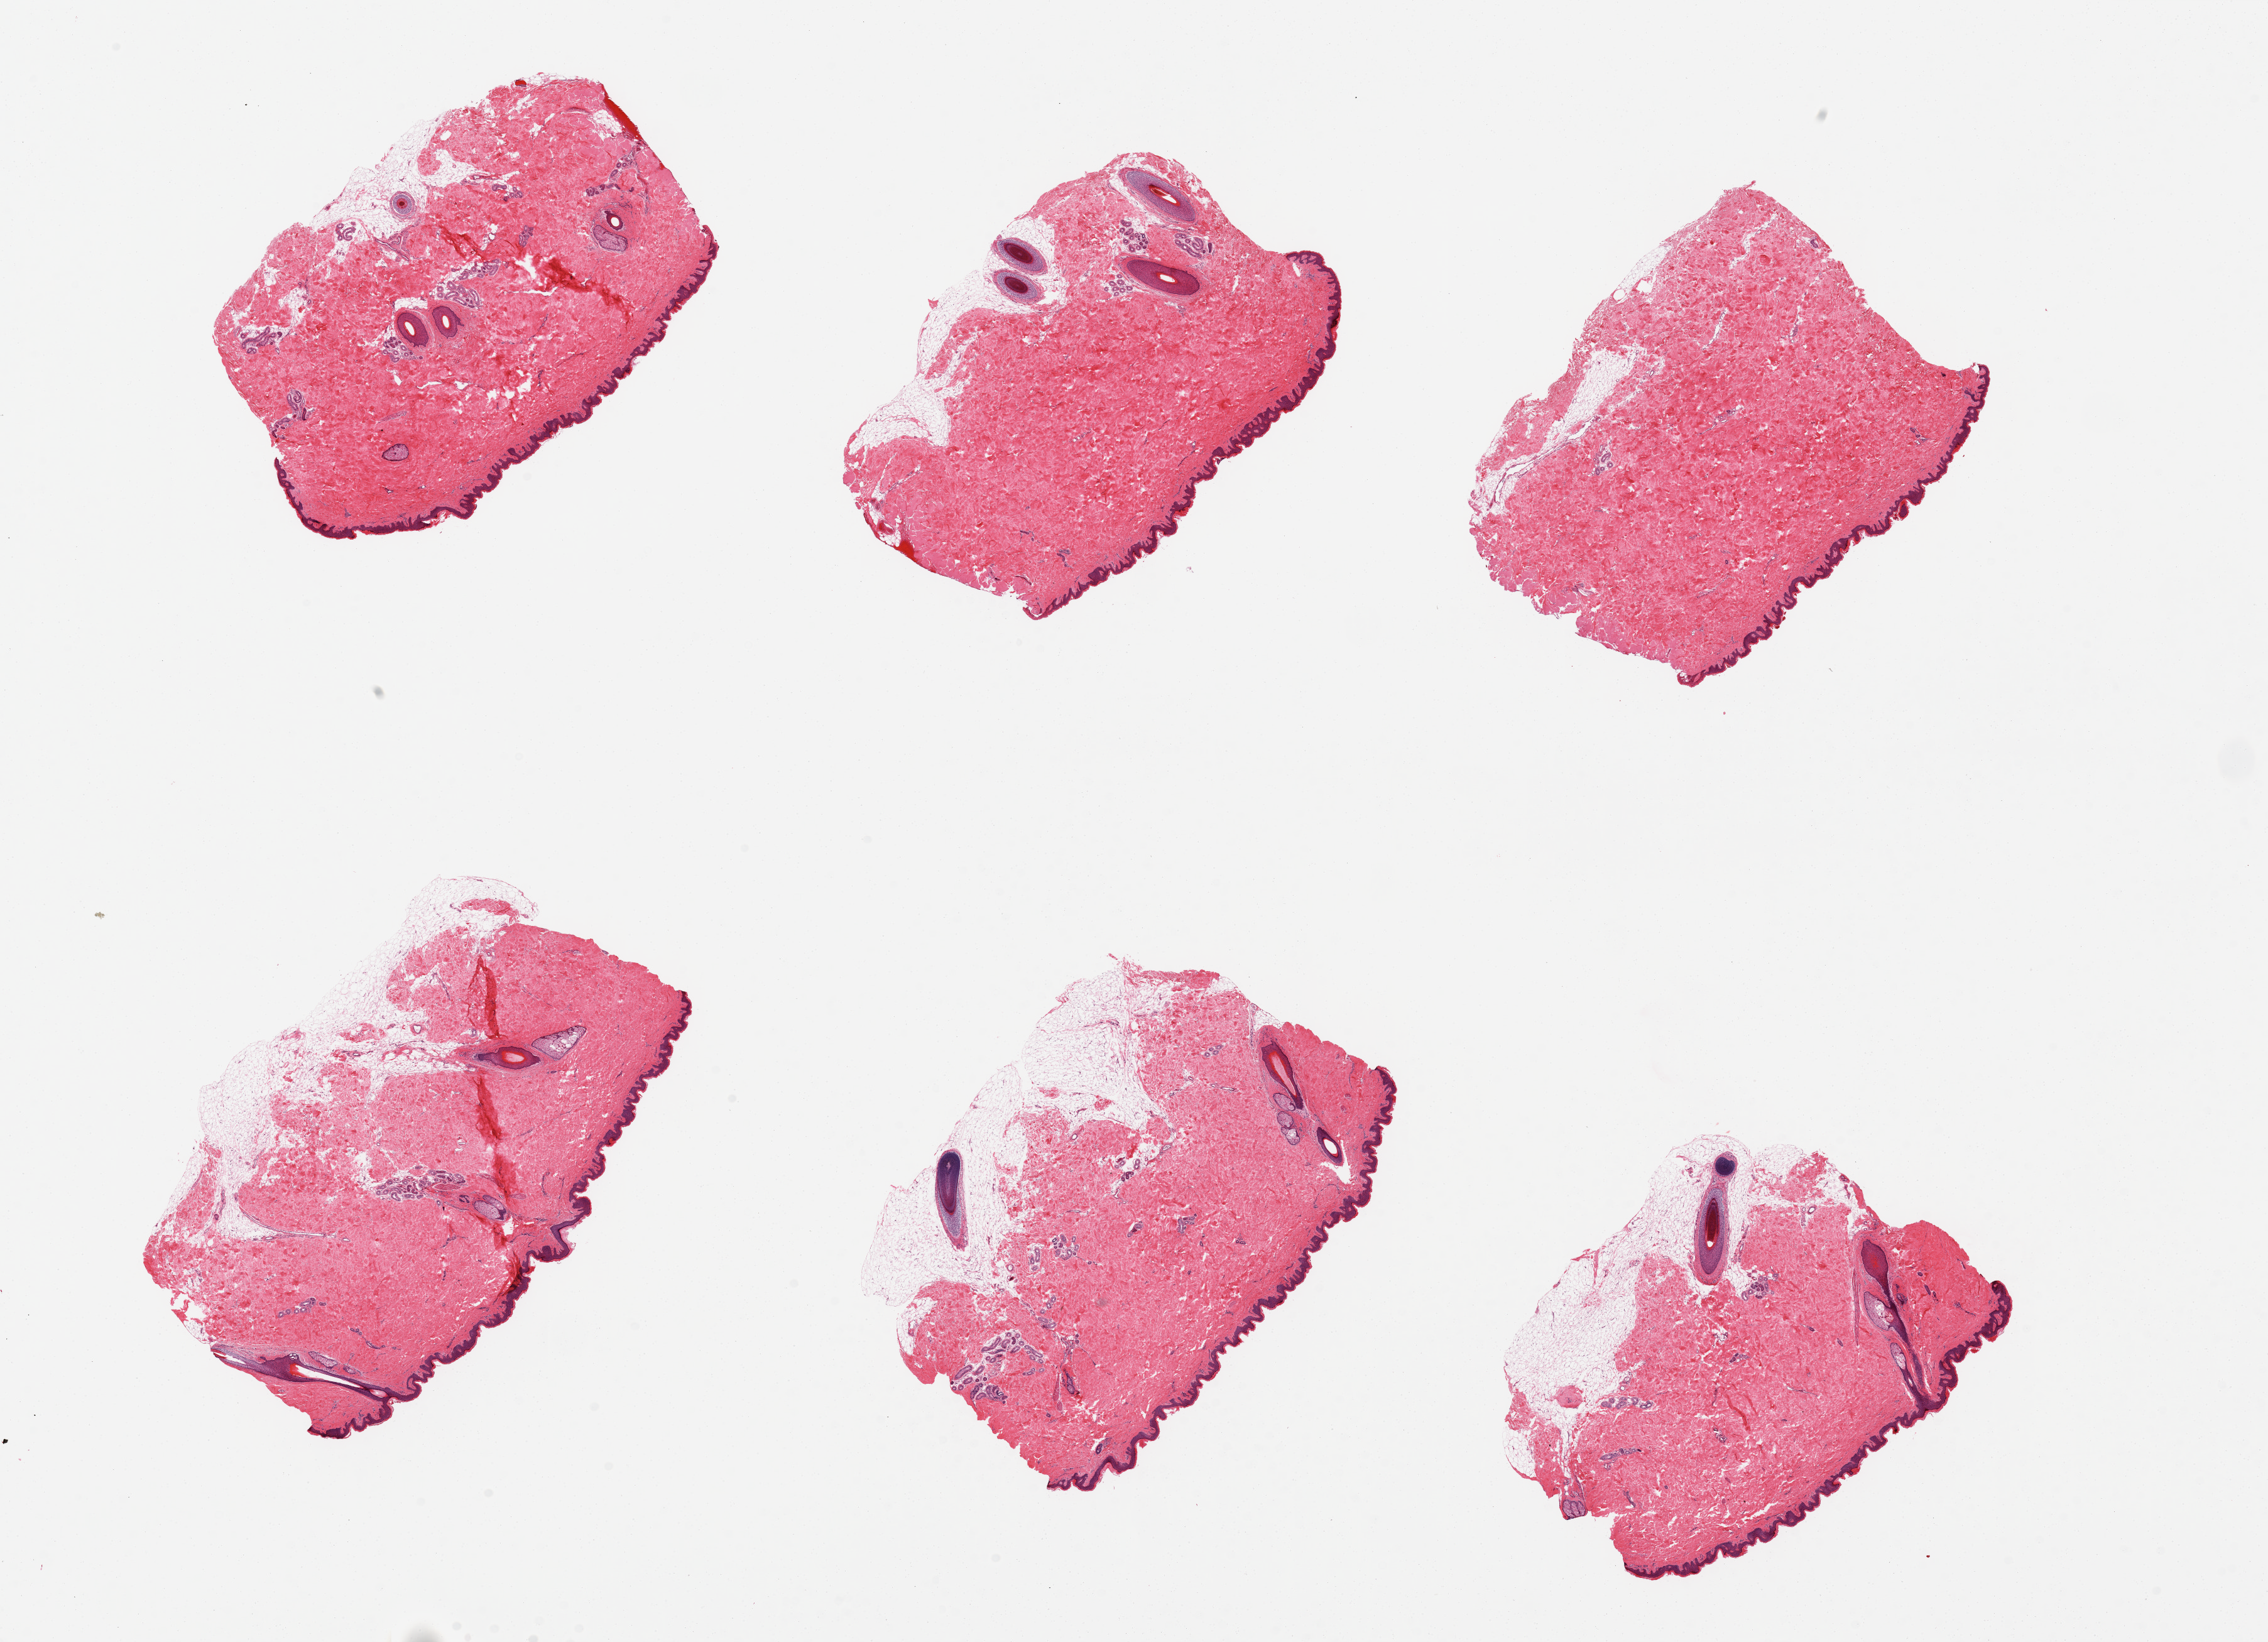
Digitized haematoxylin and eosin-stained section, brightfield, a low-resolution overview of the entire scanned area, about 28.5 x 20.7 mm; PAXgene-fixed paraffin-embedded (PFPE) section; sampled site (target tissue): skin of suprapubic region; donor tissue sample. Donor: male.
Reviewer comment on this tissue sample: 6 pieces; hair-bearing skin.